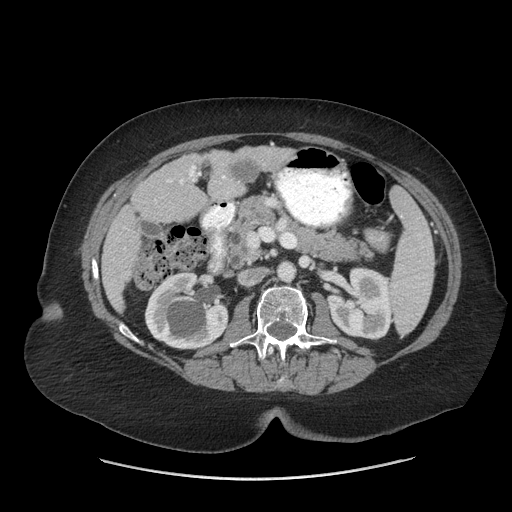
Contrast-enhanced abdominal CT (liver protocol), one axial slice. Slice 22 of 69 in the series (ordered by position). Reconstruction kernel STANDARD. 140 kVp. Soft-tissue window (W 400 / L 40 HU). 2.5 mm slice thickness. 512 × 512 image matrix, field of view 420 × 420 mm. From the clinical record (not read from this slice): diagnosis: hepatocellular carcinoma (patient treated with transarterial chemoembolisation; whether this scan precedes or follows treatment is not stated here); TNM stage (as recorded): Stage-IIIB; Child-Pugh class: A; tumour differentiation: moderately differentiated.
Outlined on this slice (semi-automatic segmentation, software-assisted and operator-edited):
- liver parenchyma outside the tumour (the mass and vessels are separate outlines, so this box may not span the whole liver): box from (x=102, y=144) to (x=292, y=310) px
- liver vessels: (x=167, y=165)–(x=226, y=184)